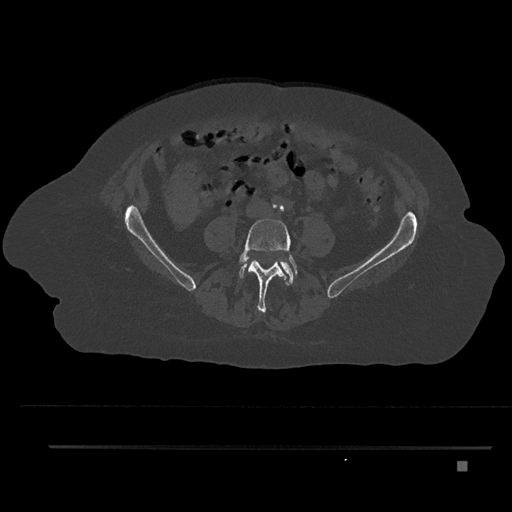
CT including the spine, one axial slice. Slice 75 of 797 in the series (ordered by position). Reconstruction kernel Br40s/3. 120 kVp. Bone window (W 1800 / L 400 HU). 0.5 mm slice thickness. 512 × 512 image matrix, field of view 437 × 437 mm. Female patient, age 76 years. Case-level facts recorded for this patient, not image findings: primary cancer: lung.
Structures marked on this image (semi-automatically segmented with operator editing):
- L4 vertebra: bounding box <237,218,298,313> (left, top, right, bottom; pixels)
- L5 vertebra: <239,260,297,285>